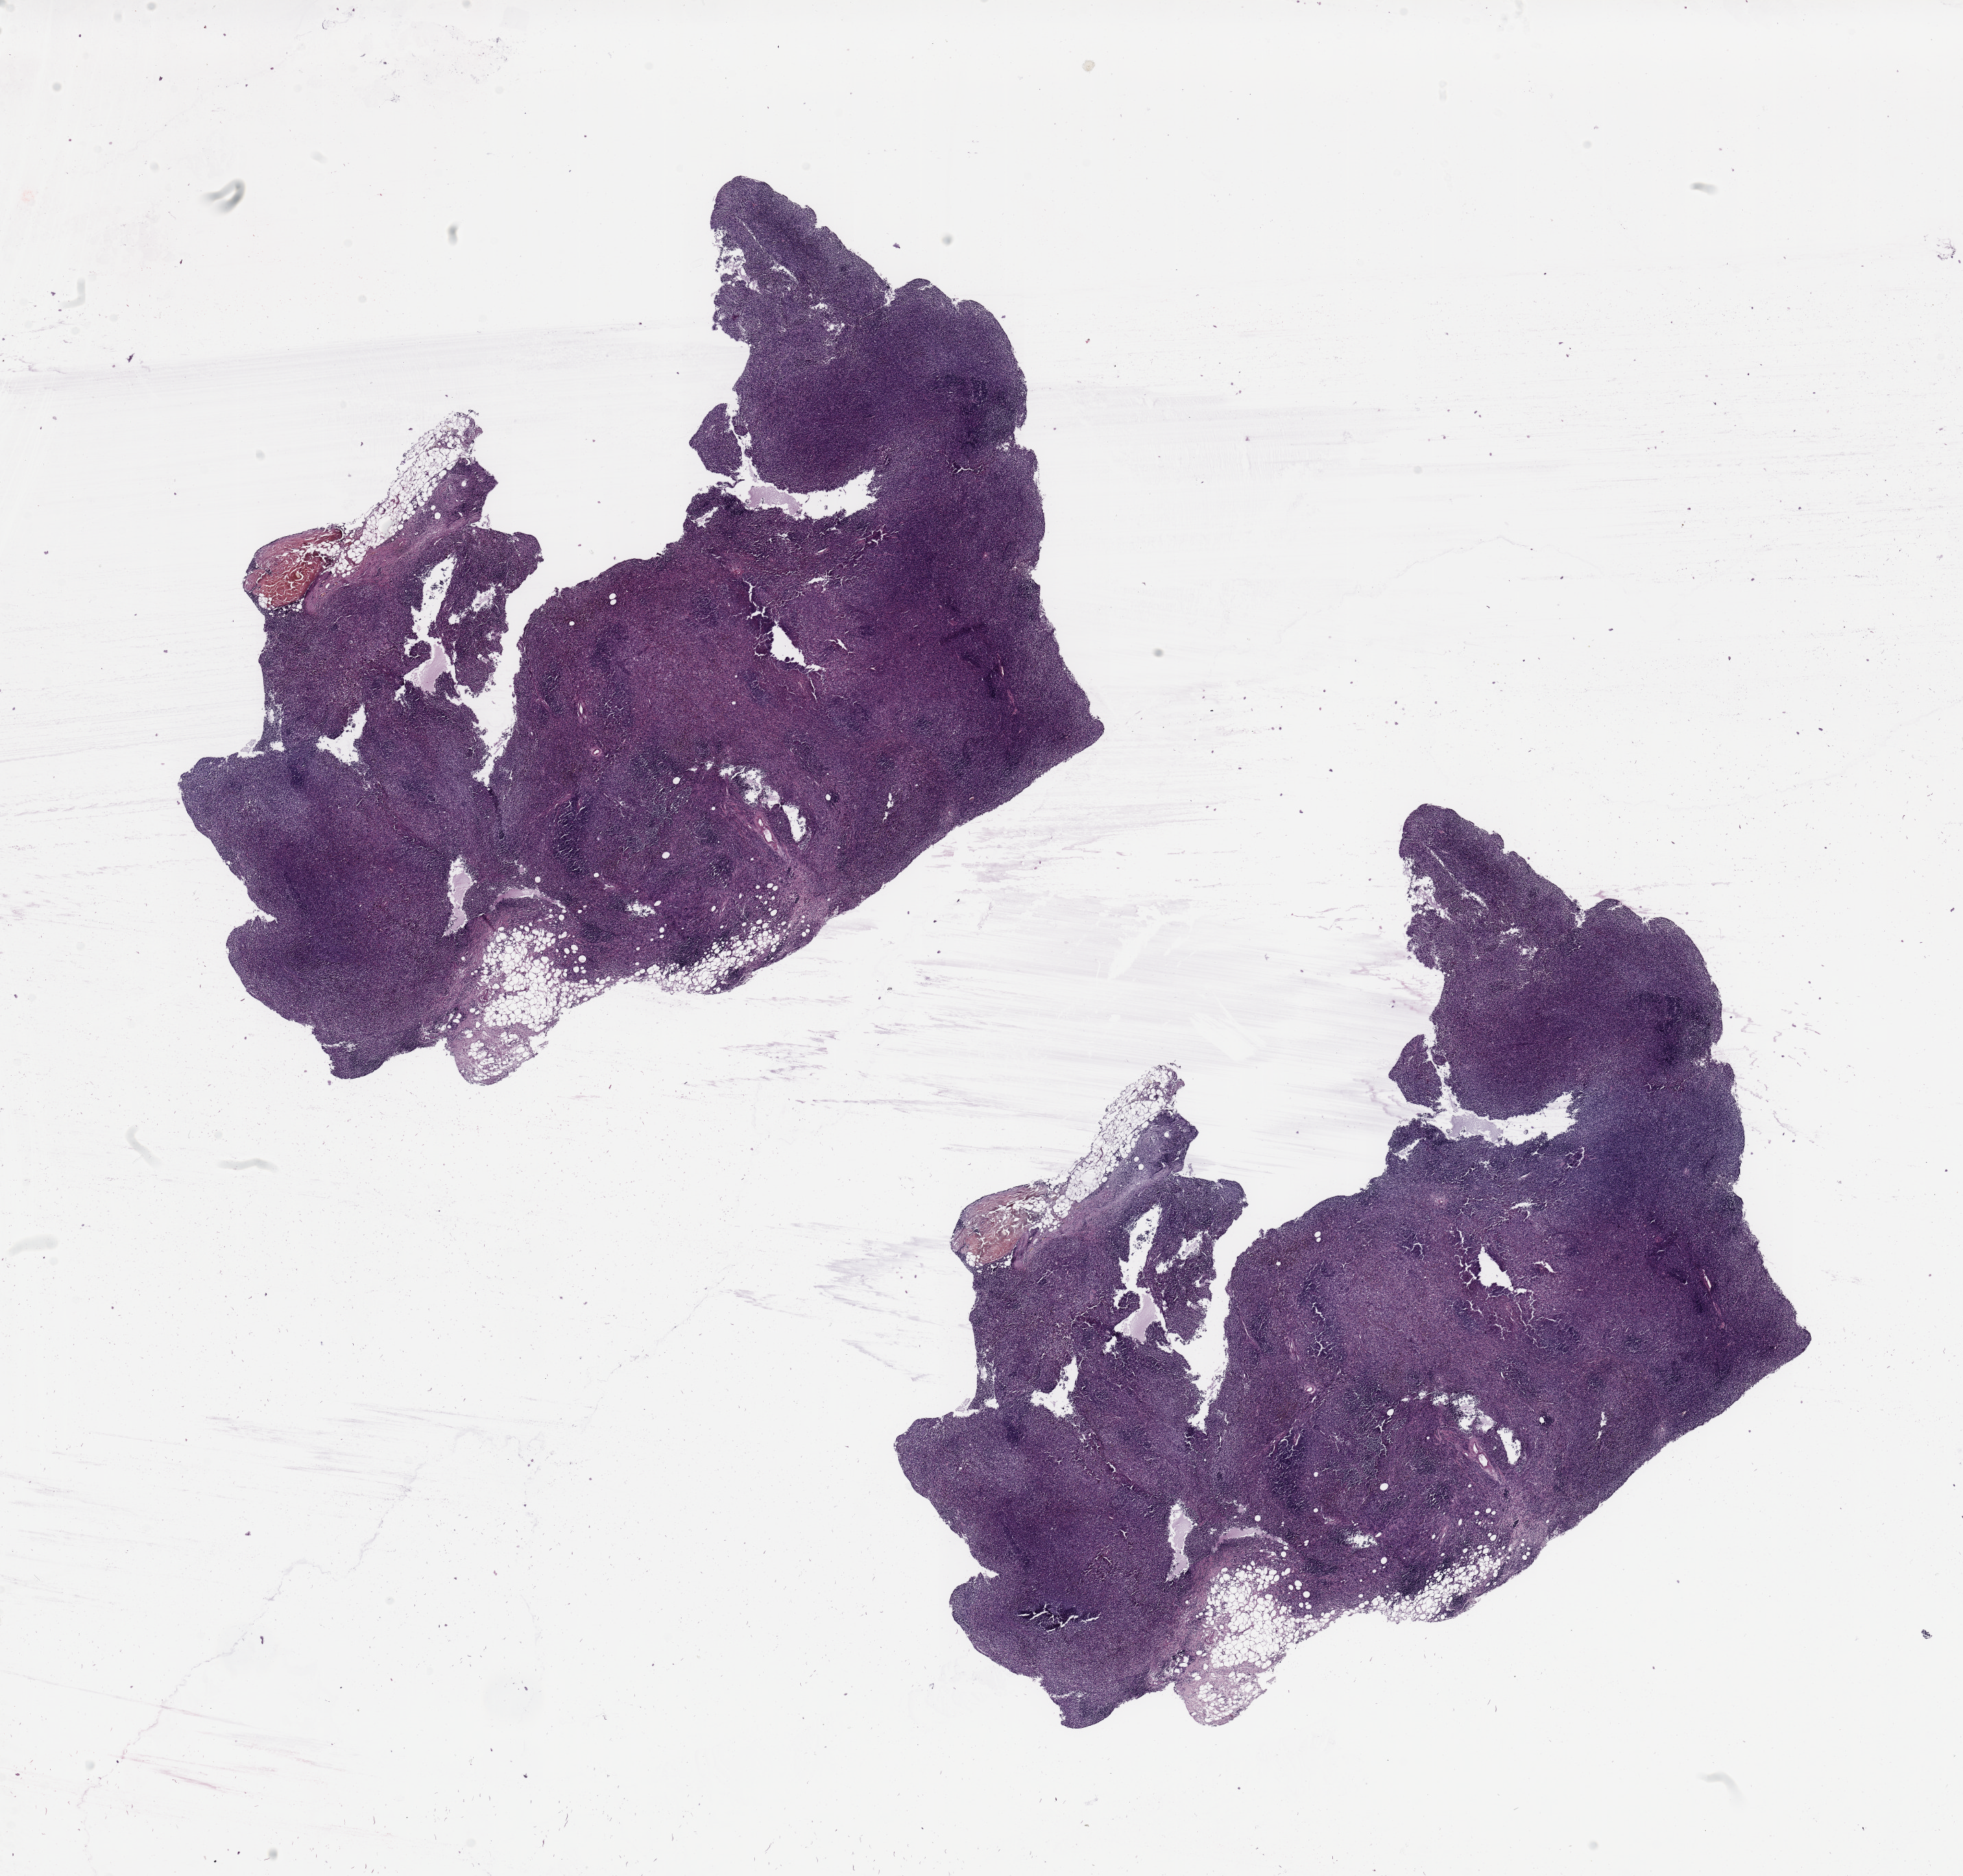
Hematoxylin and eosin (H&E) stained whole-slide image — whole scanned area (about 22.6 x 21.6 mm, slide scanned at 20x) shown as a low-resolution overview, melanoma tumour tissue; sampled site not recorded. 77-year-old male patient.
- AJCC pathologic stage: IA
- histologic diagnosis: Malignant melanoma, NOS